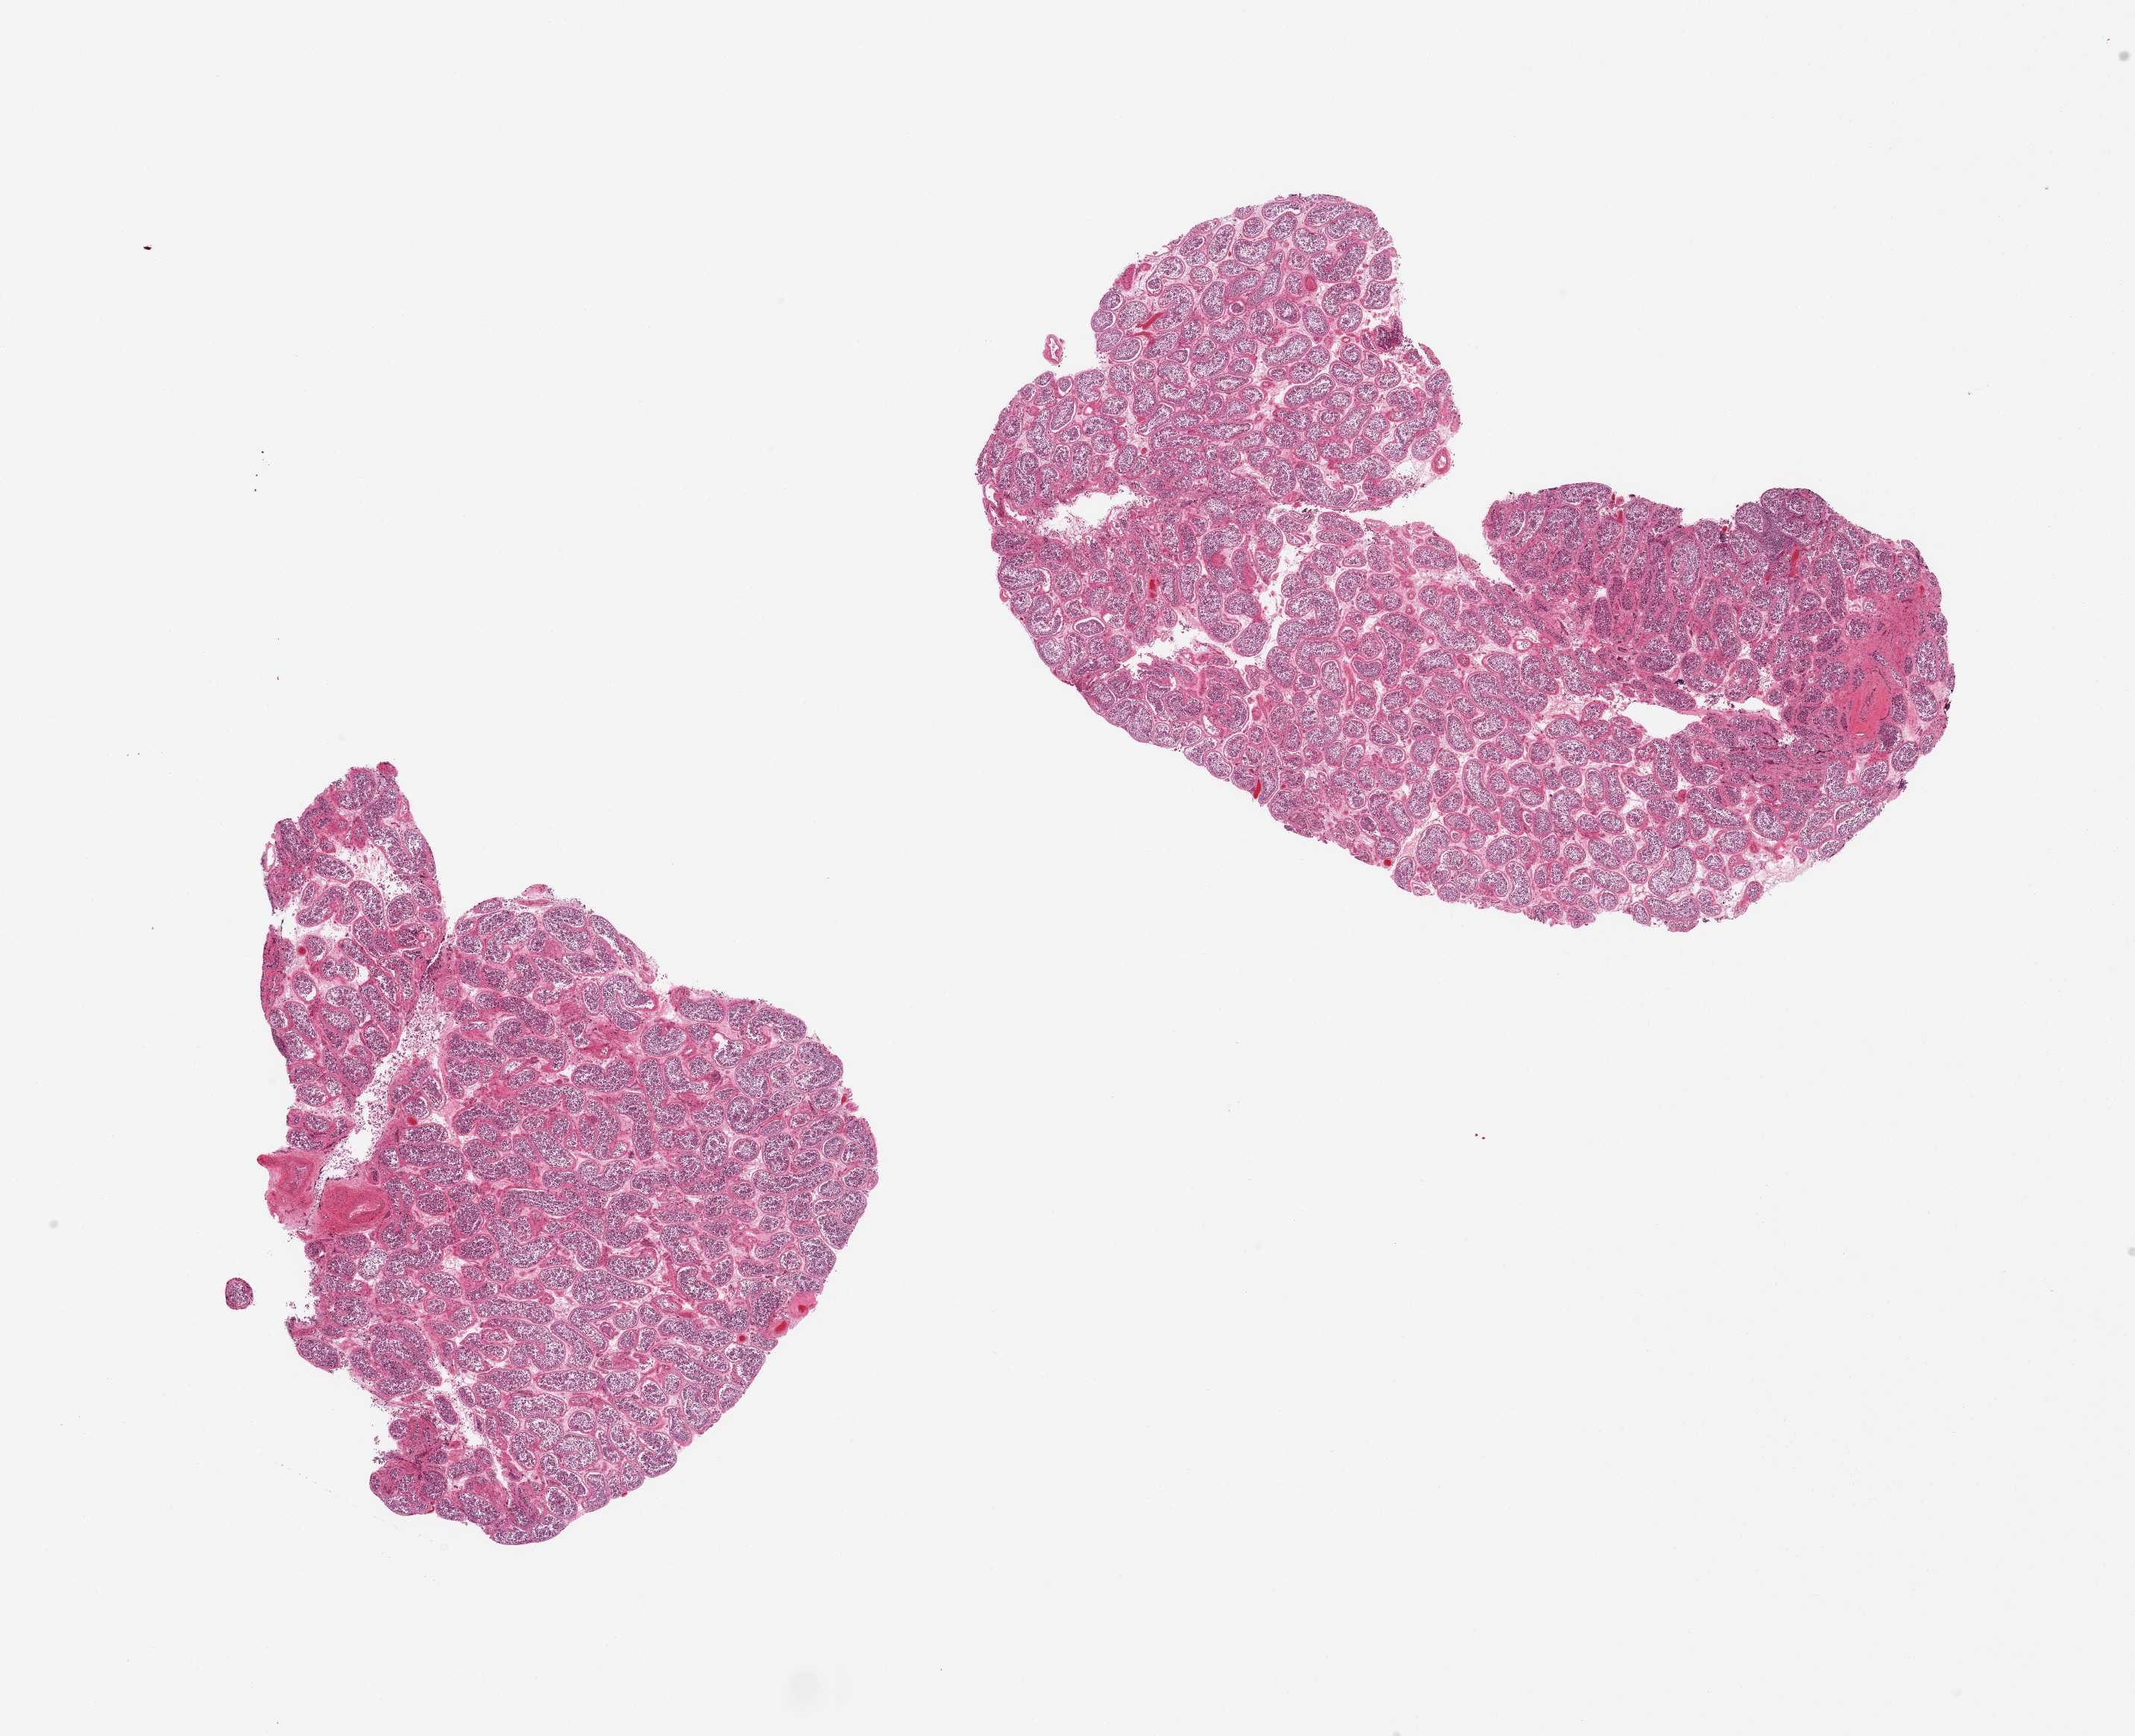
Whole-slide image, haematoxylin and eosin stain, brightfield, shown as a low-resolution overview of the whole scanned area (about 22.6 x 18.4 mm, from a 20x scan). PAXgene-fixed paraffin-embedded (PFPE) section. Target tissue: testis. Tissue donor sample.
* review note (as recorded): 2 pieces, spermatogenesis appears reduced